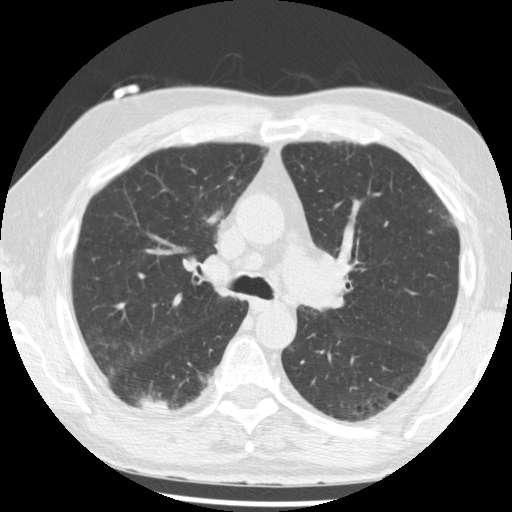
Low-dose screening chest CT, one axial slice. Slice 136 of 221 in the series (ordered by position). Lung window (W 1500 / L -600 HU). 2.5 mm slice thickness. 512 × 512 image matrix.
Structures marked on this image (expert manual segmentation):
- lesion 1 (tumor, lower lobe of right lung): bounding box [x1, y1, x2, y2] px = [140, 396, 172, 412]